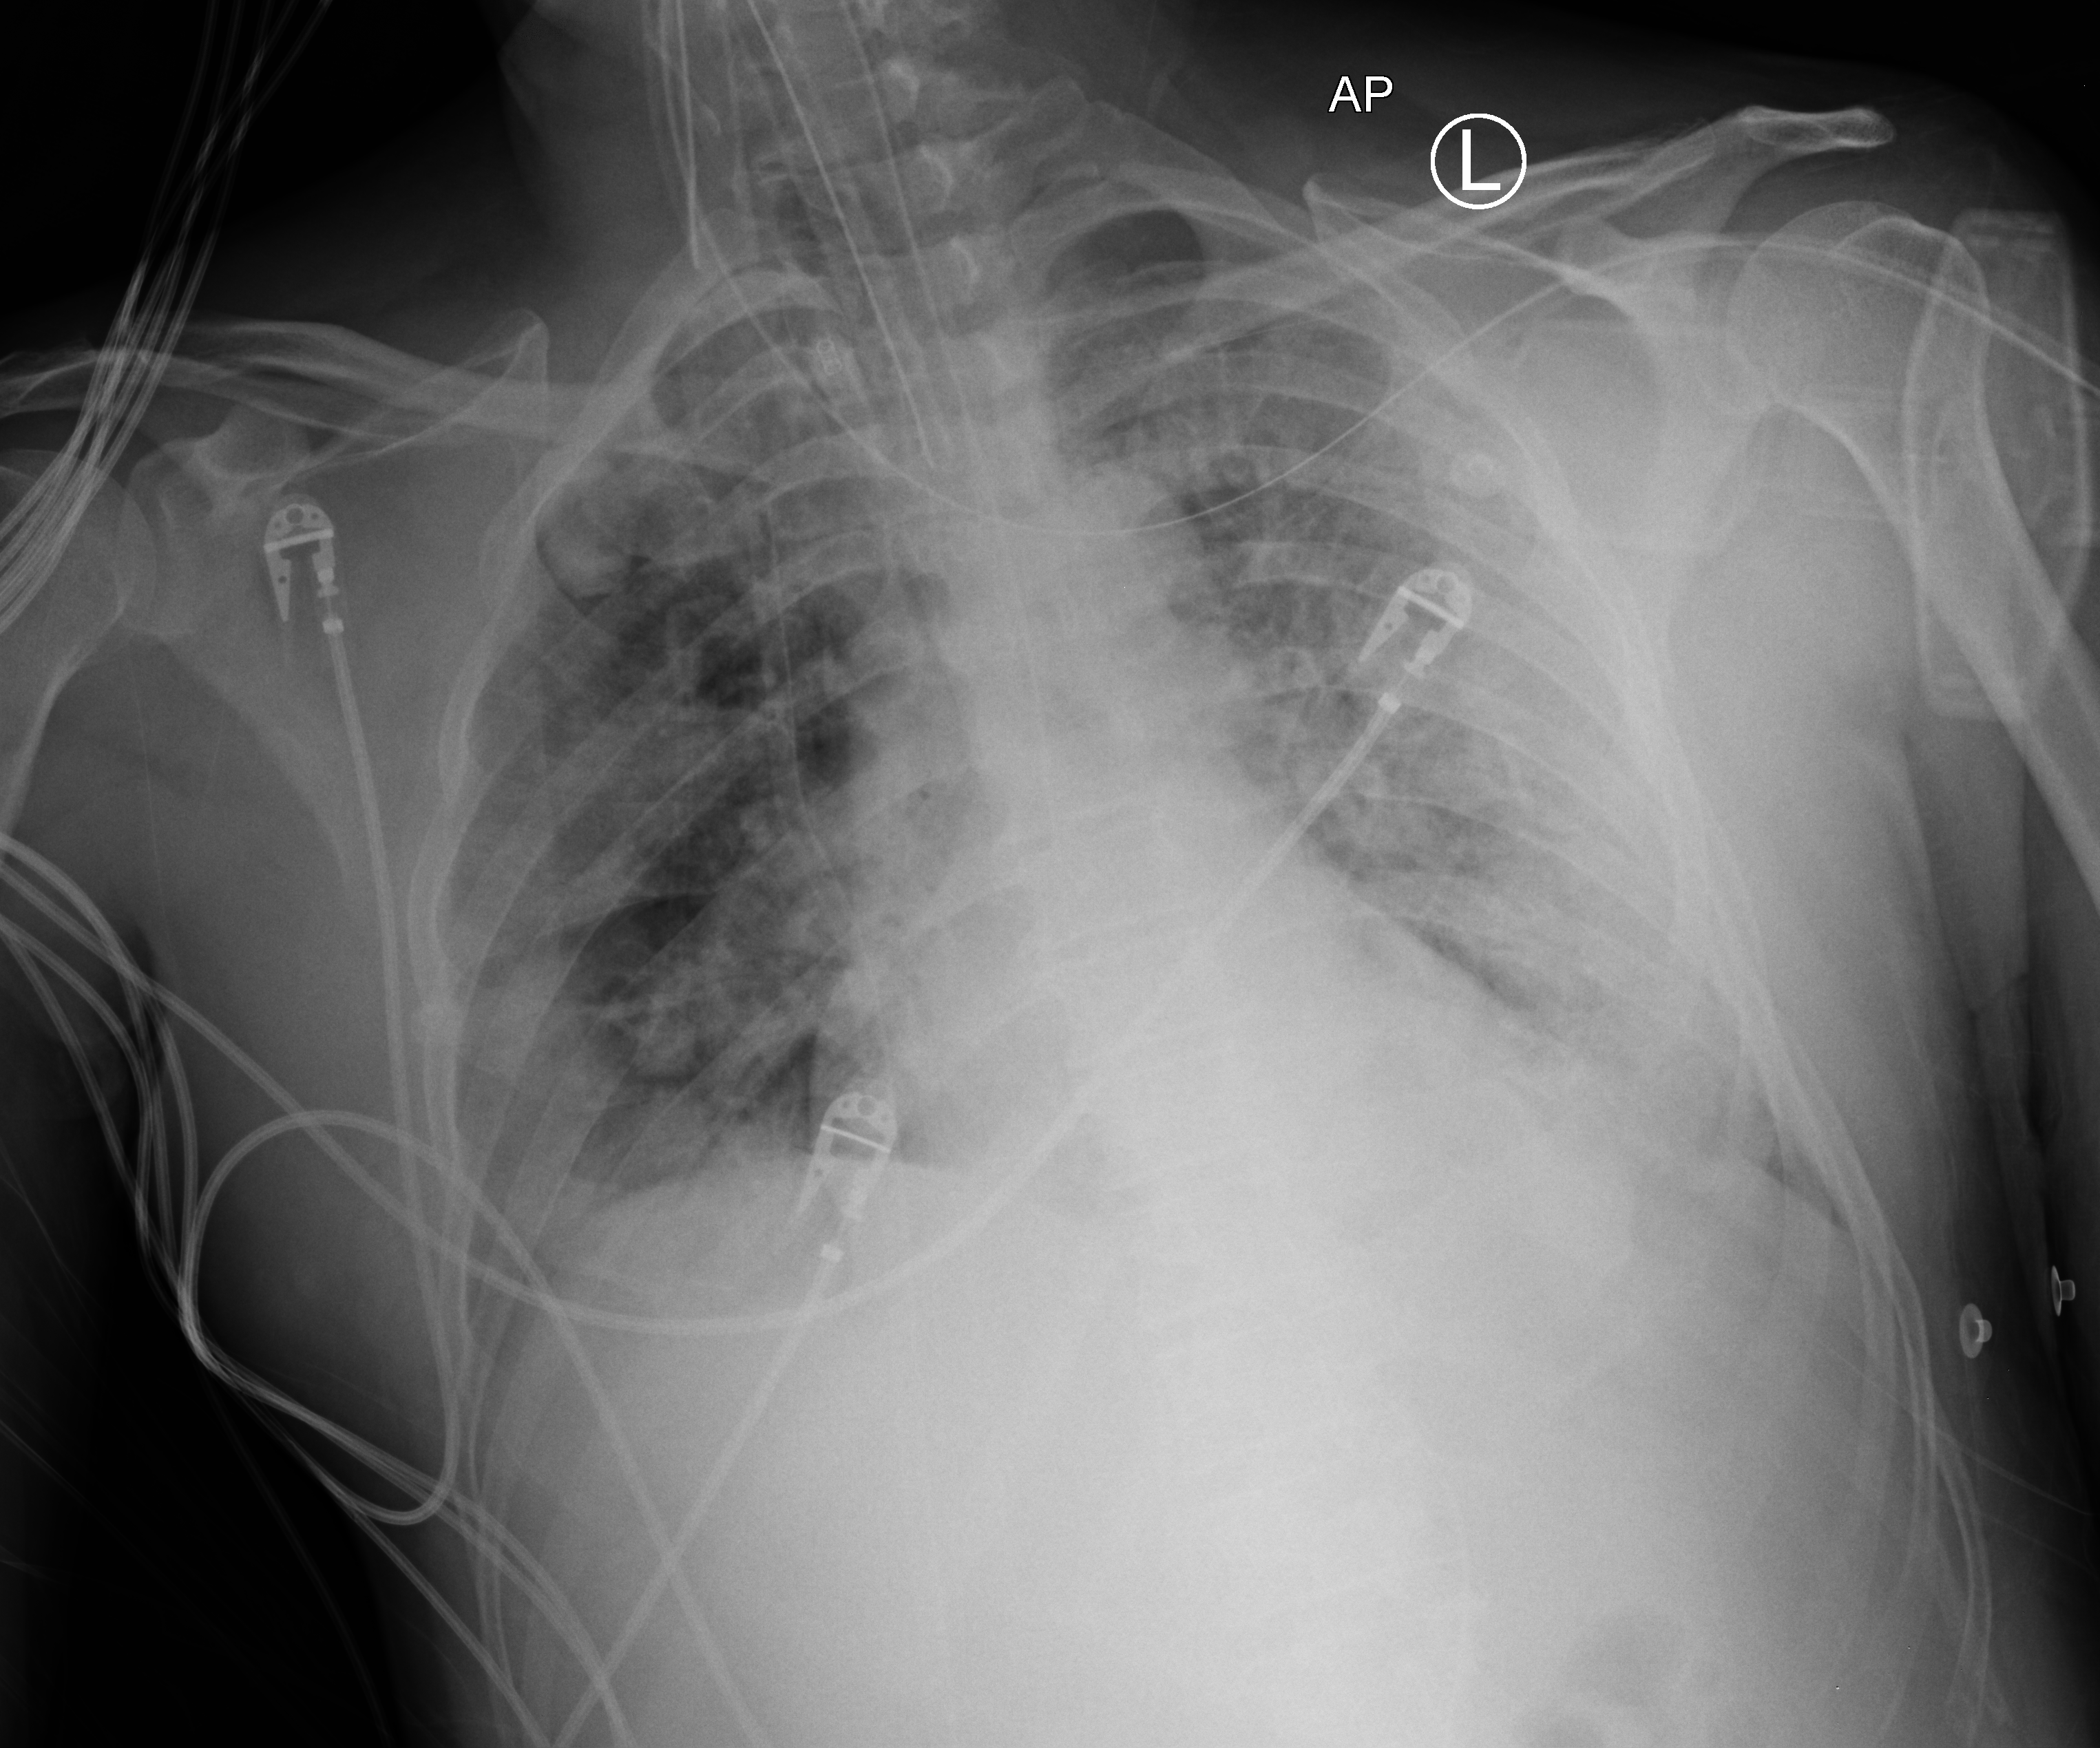
Bedside chest radiograph (computed radiography). Patient hospitalised with COVID-19; male, aged 18–59 years.
Admission-level facts for this patient (not findings on this image; timing relative to this image not recorded): mechanically ventilated during this hospital stay: yes; chronic kidney disease (admission record): no; COPD (admission record): no.